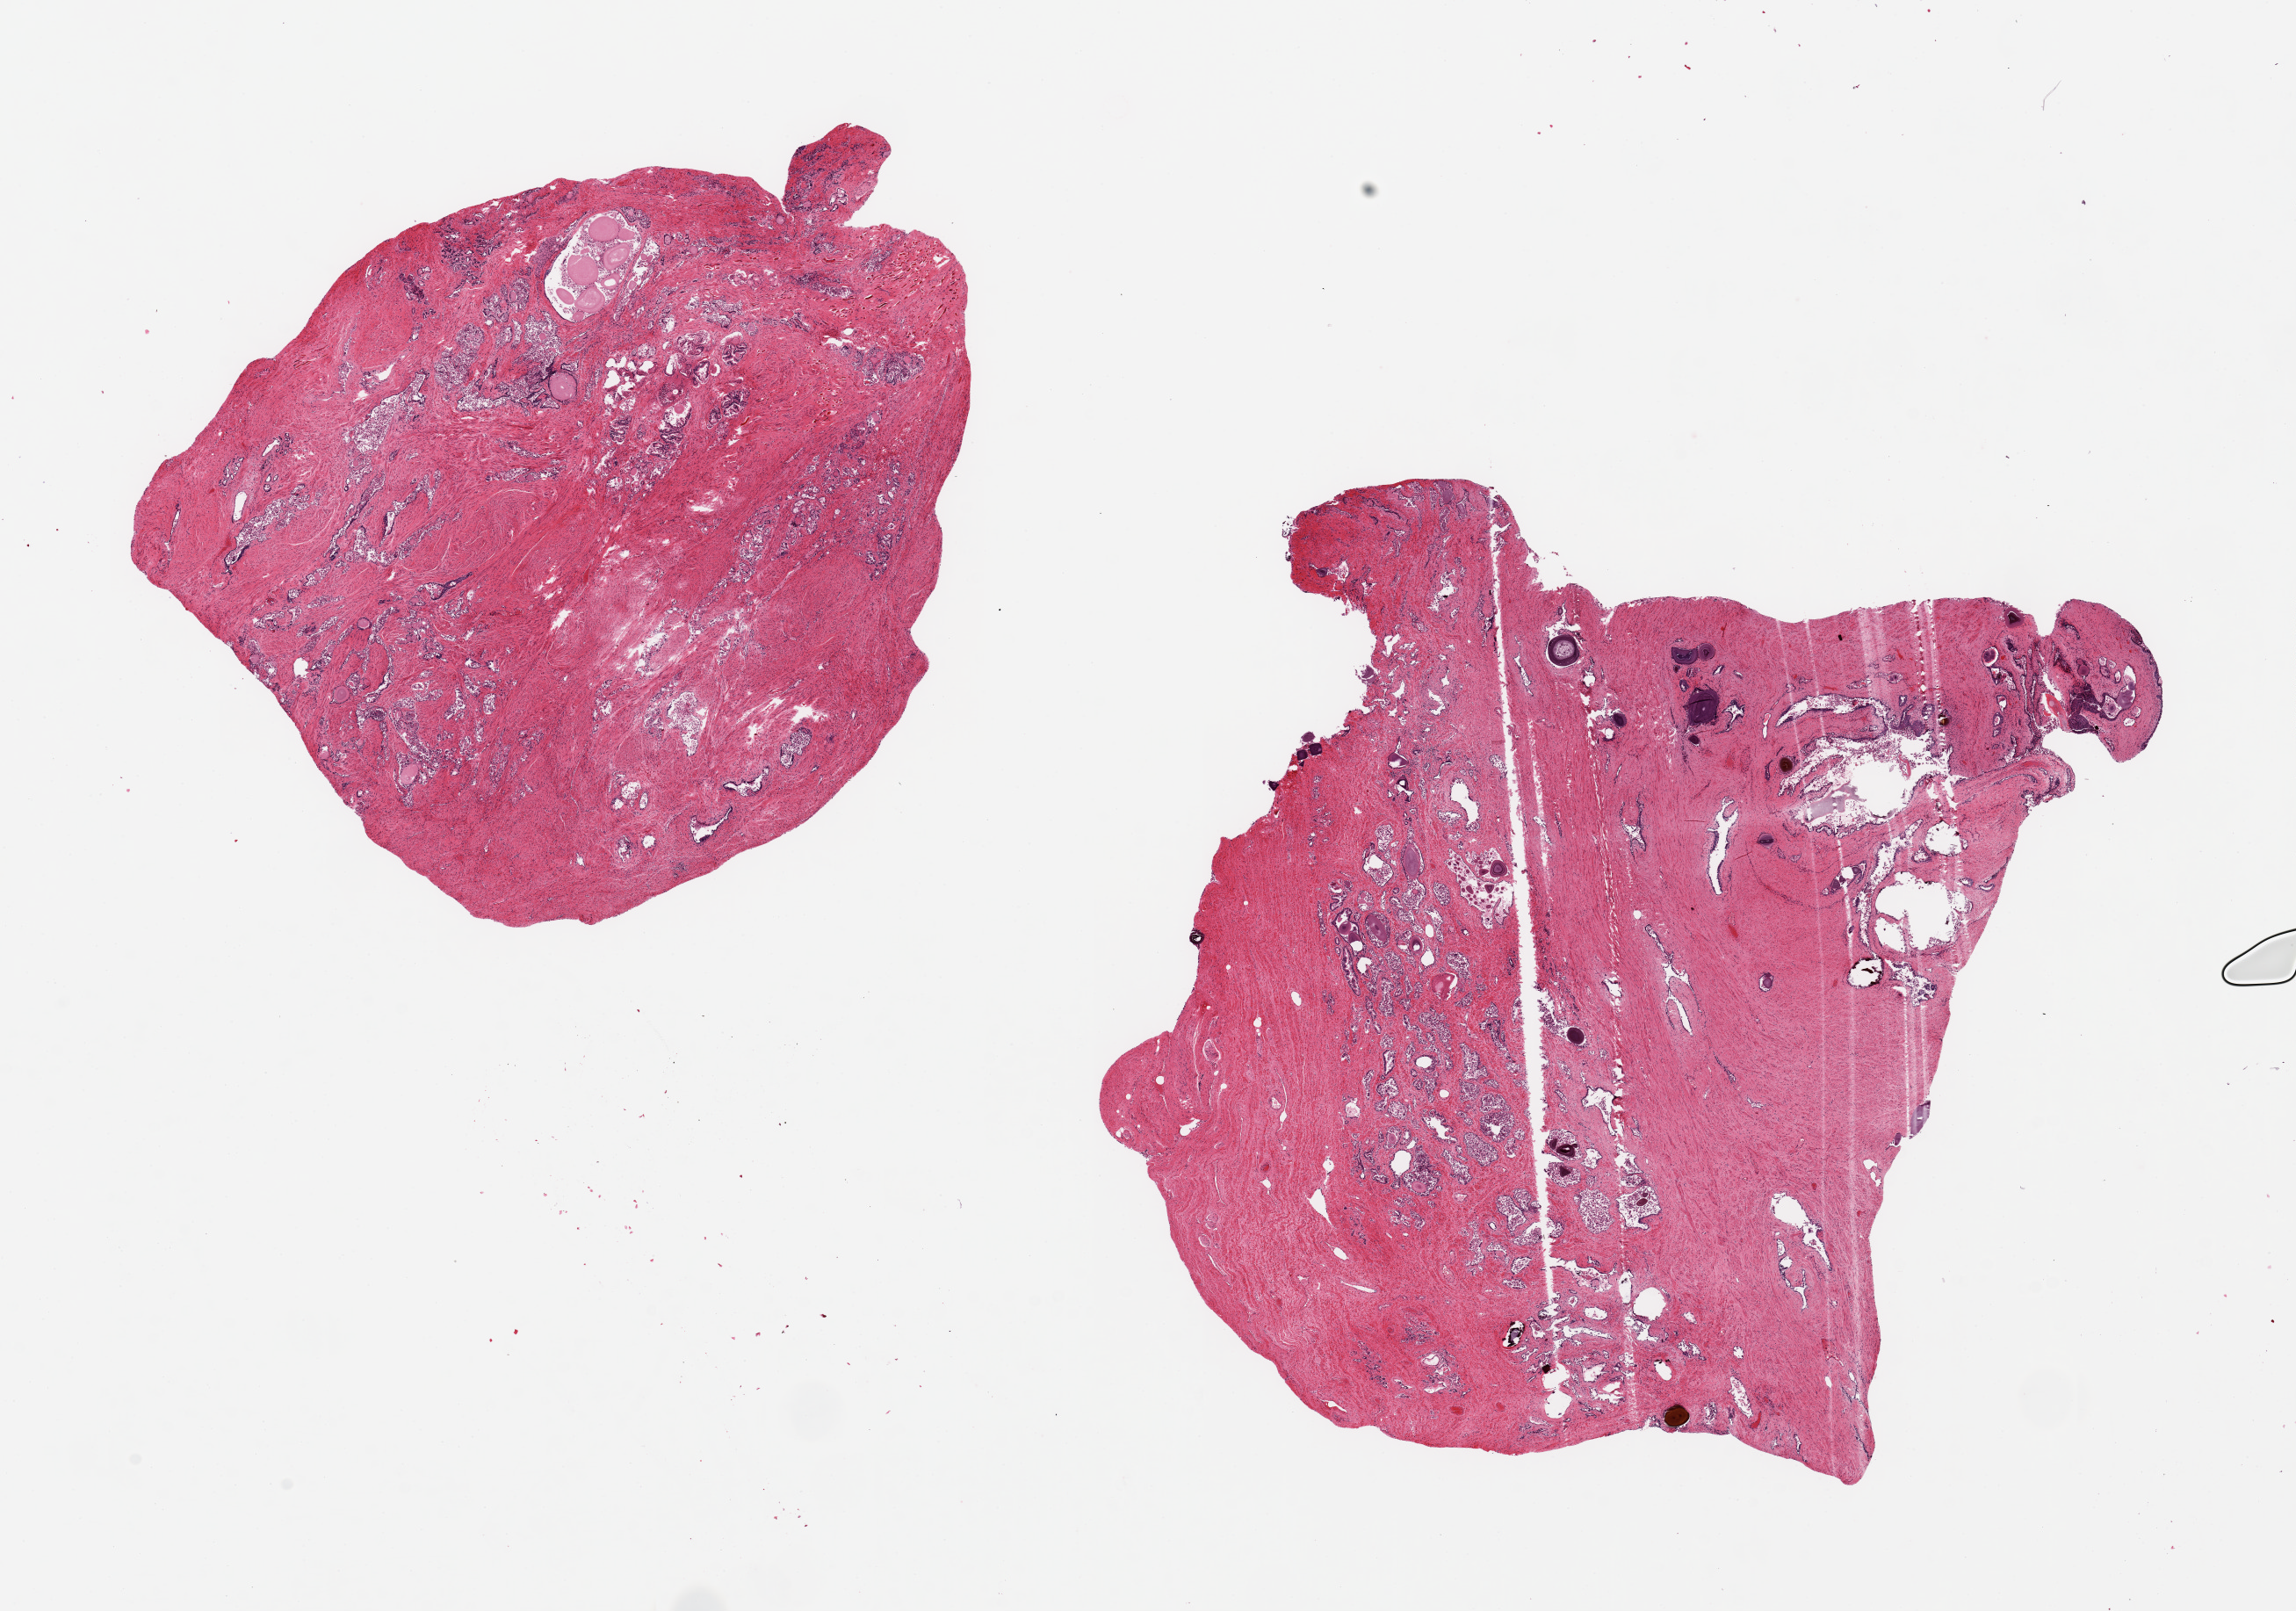
Hematoxylin and eosin (H&E) whole-slide image, shown as a low-resolution overview of the whole scanned area (about 20.7 x 14.5 mm), PAXgene-fixed, paraffin-embedded tissue, sampled site (target tissue): prostate, donor tissue sample. Donor: male.
- review note (as recorded): 2 pieces, 8x6 & 8x8mm; glands largely autolyzed; muscle appears preserved